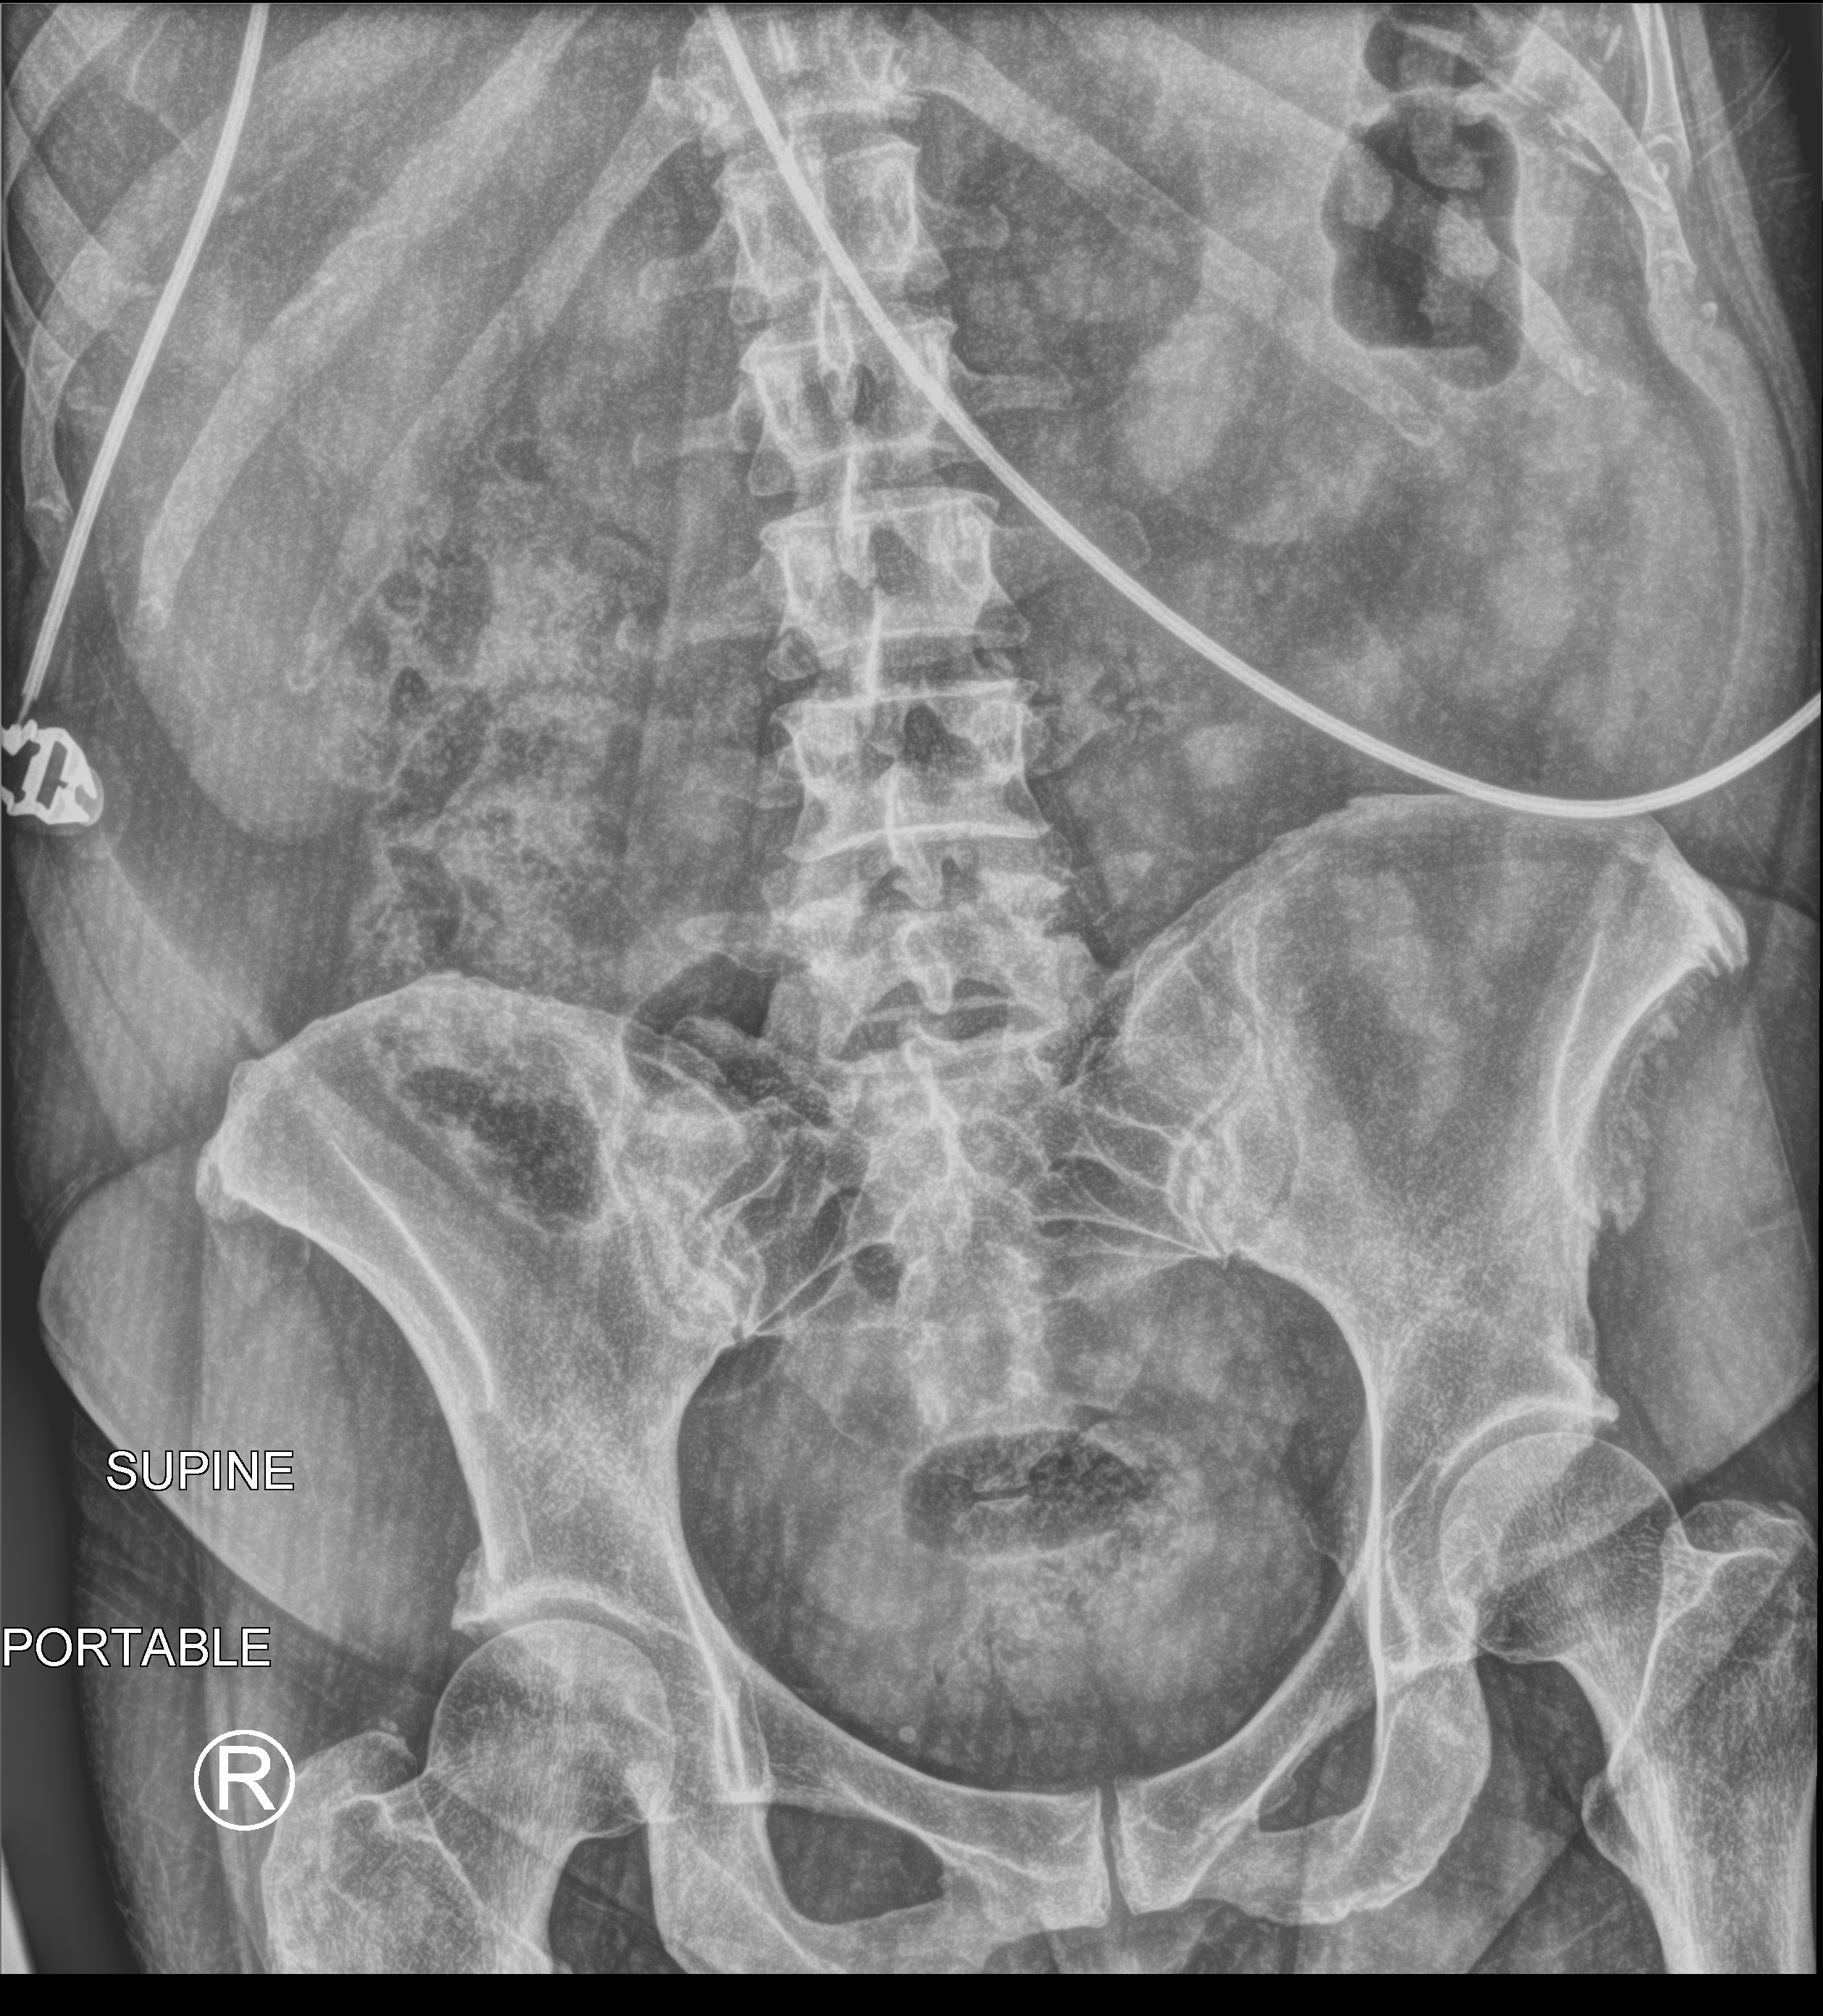
Bedside abdomen radiograph (computed radiography); anteroposterior (AP) projection. Patient hospitalised with COVID-19; female, aged 18–59 years.
Admission-level facts for this patient (not findings on this image; timing relative to this image not recorded):
- chronic kidney disease (admission record): no
- hypertension (admission record): no